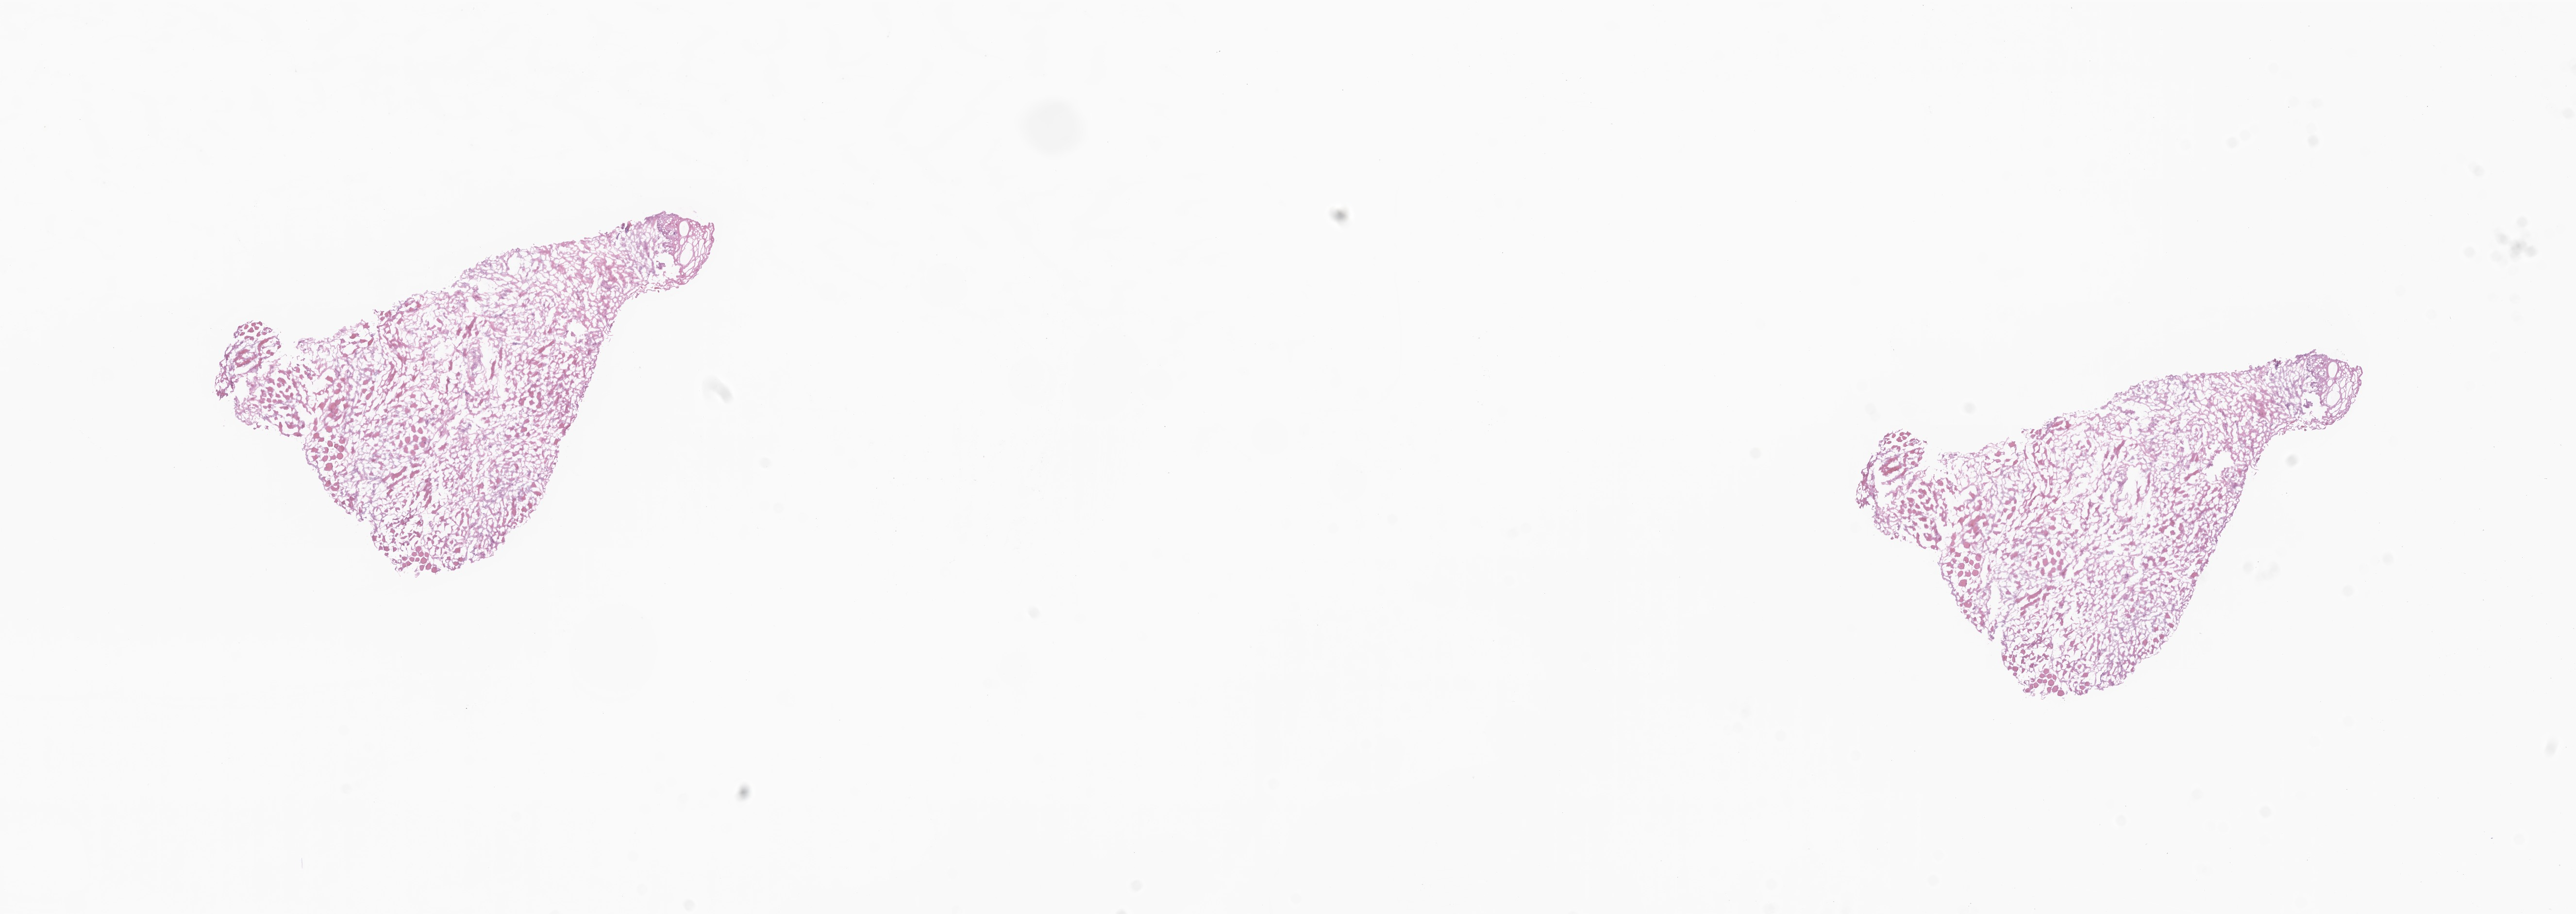
Whole-slide image, H&E stain — low-resolution overview of the scanned area, about 22.4 x 7.9 mm, frozen section, specimen: normal-tissue sample (non-tumor) from a patient with squamous cell carcinoma, NOS, site: tongue. Female patient. Pathologist review of this section (percent, as recorded): tumor cells 0%, tumor nuclei 0%, stromal cells 100%, necrosis 0%, normal cells 0%. Inflammatory infiltration, as recorded: lymphocyte infiltration 0%, monocyte infiltration 0%, neutrophil infiltration 0%.
This section: non-tumor tissue sample; the patient's diagnosis is given above.